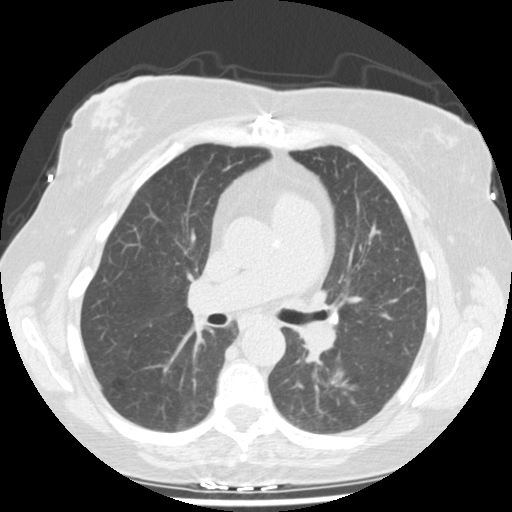
Low-dose screening chest CT, one axial slice; slice 99 of 159 in the series (ordered by position); reconstruction kernel STANDARD; 120 kVp; lung window (W 1500 / L -600 HU); 512 × 512 image matrix, field of view 326 × 326 mm.
Outlined on this slice (expert manual segmentation):
- lesion 1 (tumor, lower lobe of left lung): bounding box [x1, y1, x2, y2] px = [333, 377, 342, 378]